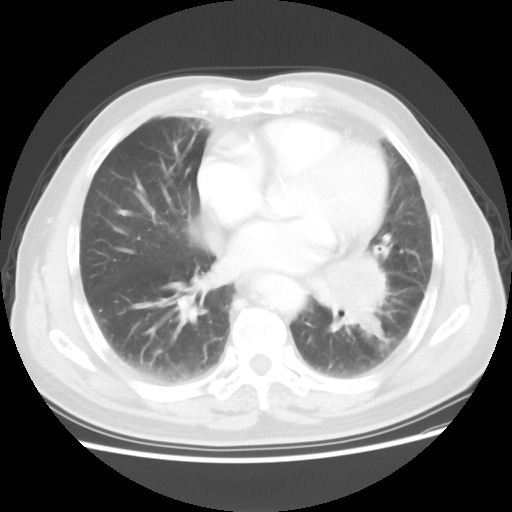
Chest CT, one axial slice. Position 26 of 56 along the scan axis. Lung window (W 1500 / L -600 HU). 5 mm slice thickness. 512 × 512 image matrix, field of view 360 × 360 mm. Patient: male, 75 years. Case-level facts recorded for this patient, not image findings: clinical TNM (as recorded): T3 N0 M0.
Outlined on this slice (rectangle marked by the reading radiologist):
- lung tumour (recorded histology: squamous cell carcinoma): bounding box [x1, y1, x2, y2] px = [308, 244, 394, 349]